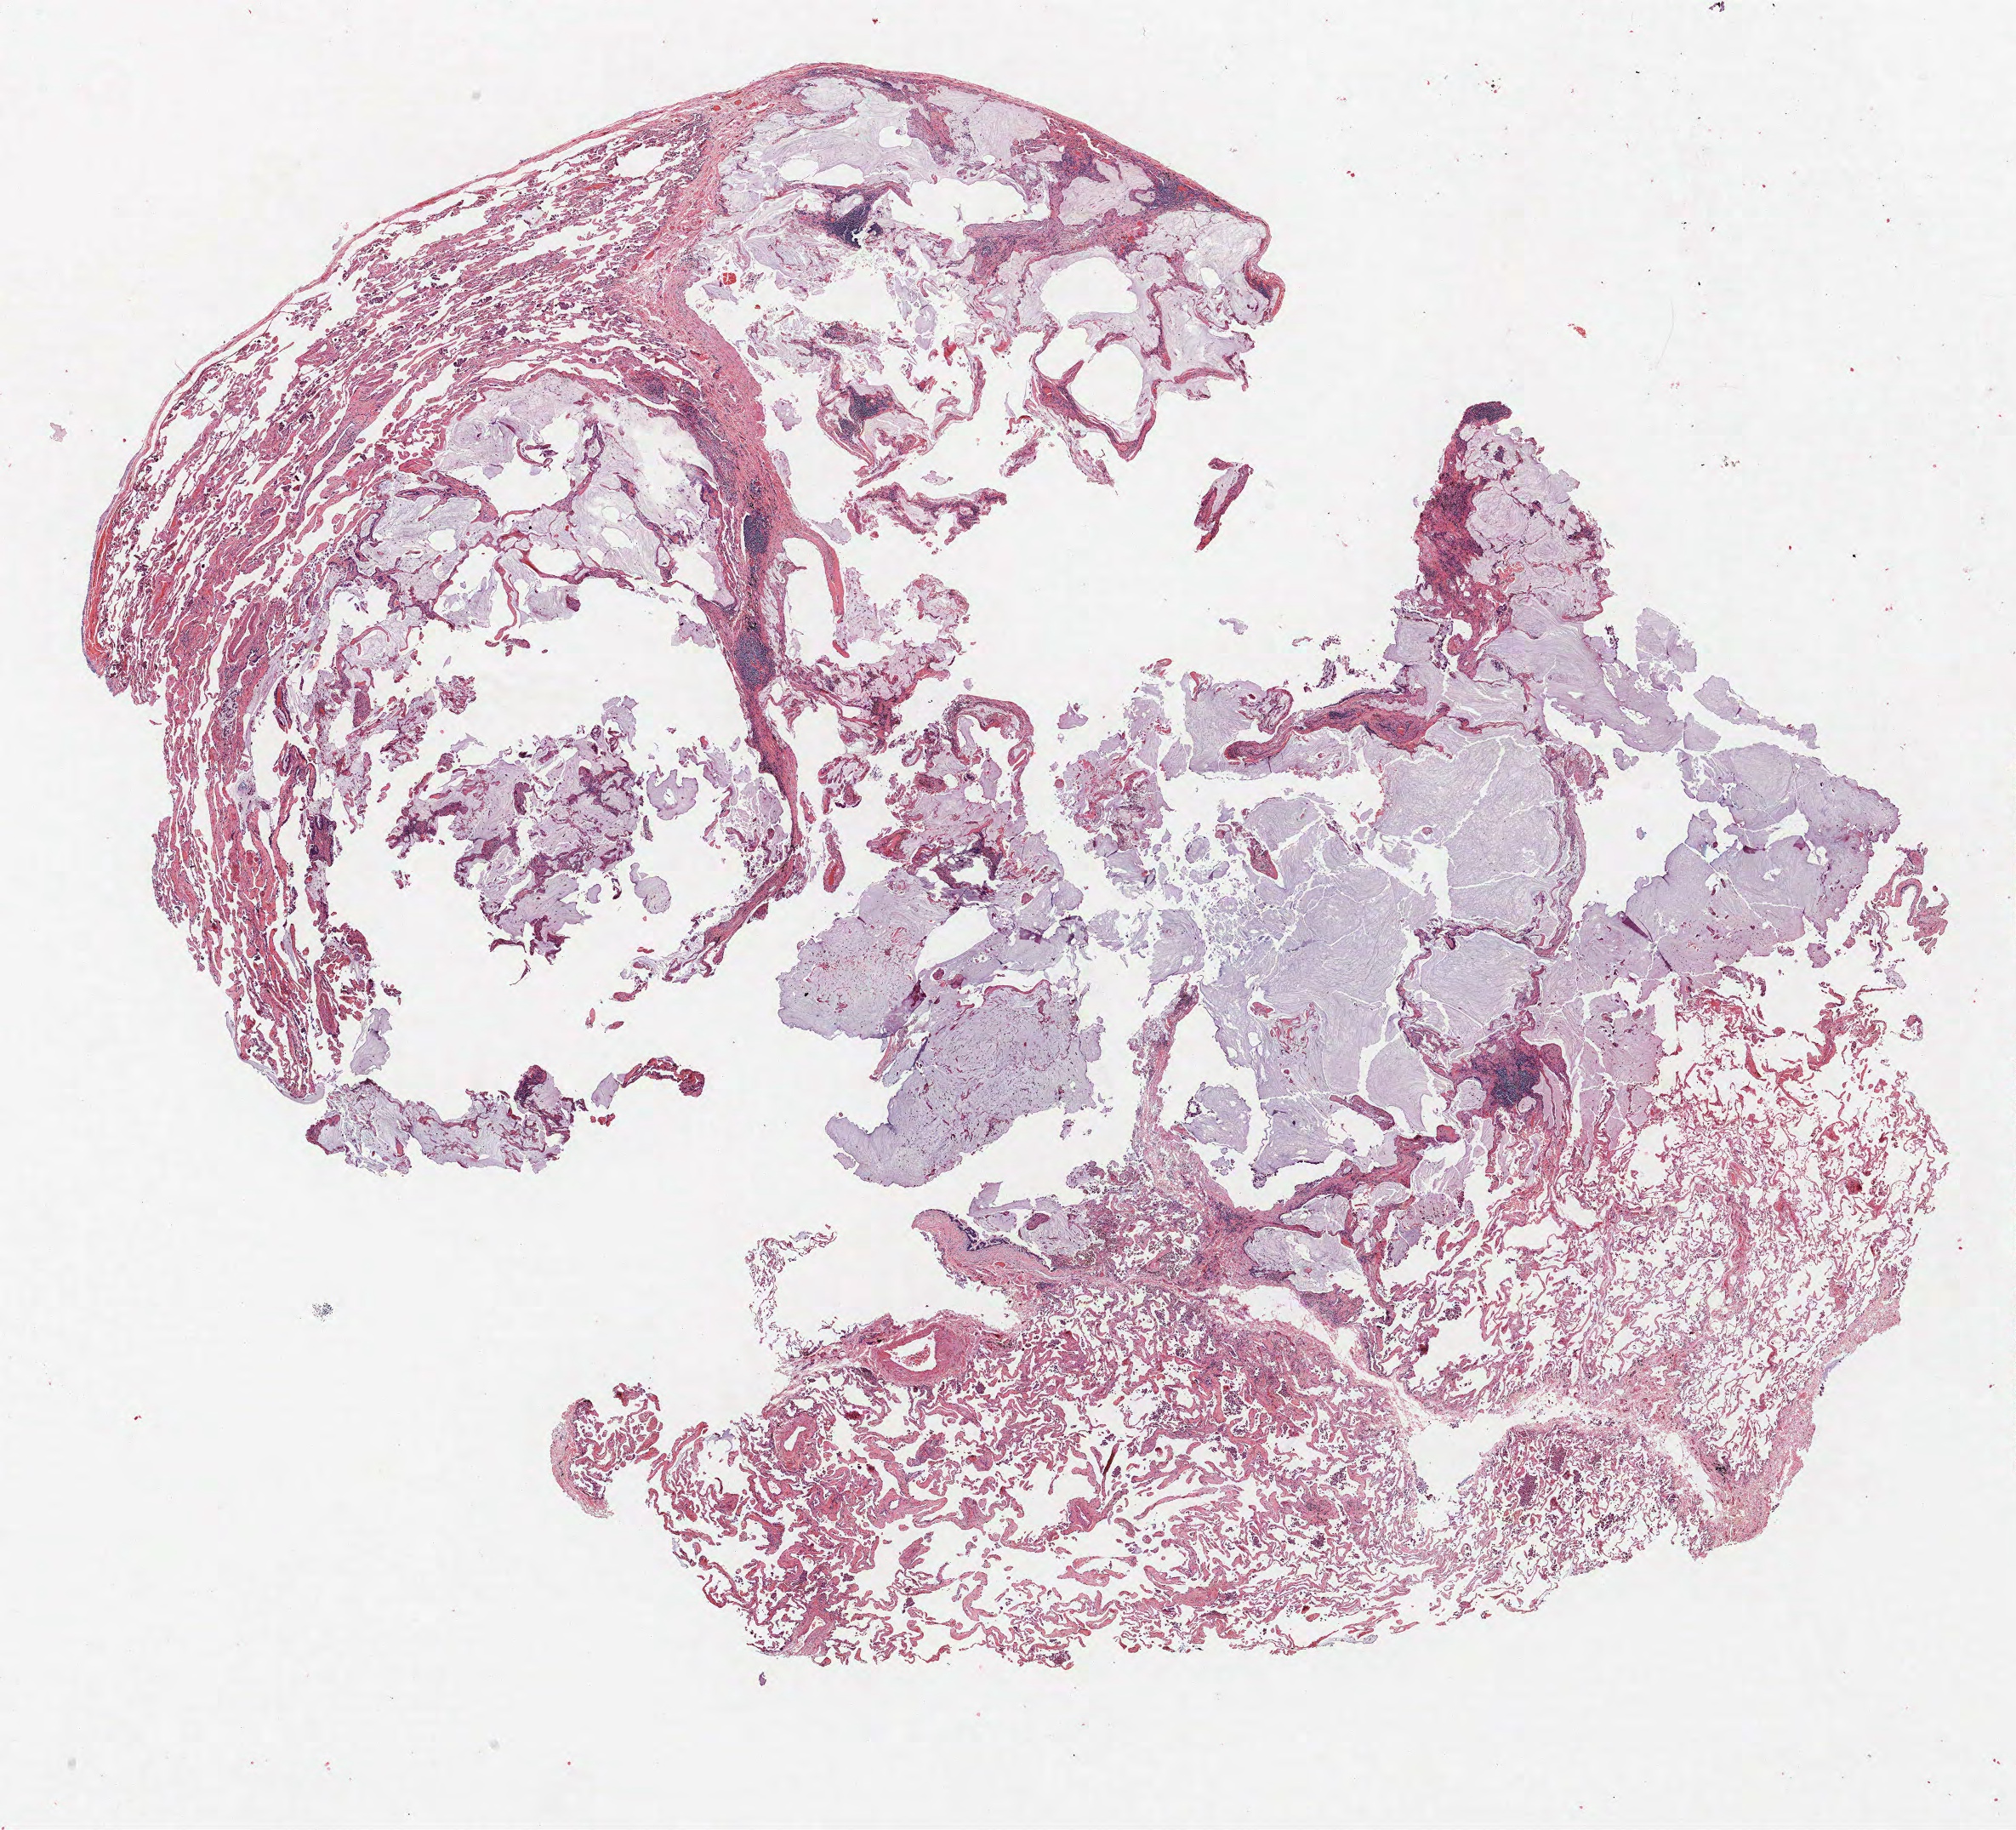
Whole-slide histology image, Hematoxylin and eosin (H&E) stained, shown as a low-resolution overview of the whole scanned area (about 19.0 x 17.2 mm, acquisition: 40x scan); FFPE section; lung. Male patient, aged 66 at enrolment. Current smoker at enrolment. Grade: well differentiated (G1).
Tumour size (pathology): 18 mm. Stage (AJCC 6th edition): IA. Primary tumour location (clinical record): left upper lobe. Participant's lung-cancer diagnosis: Bronchiolo-alveolar carcinoma, mucinous (ICD-O-3 8253/3).